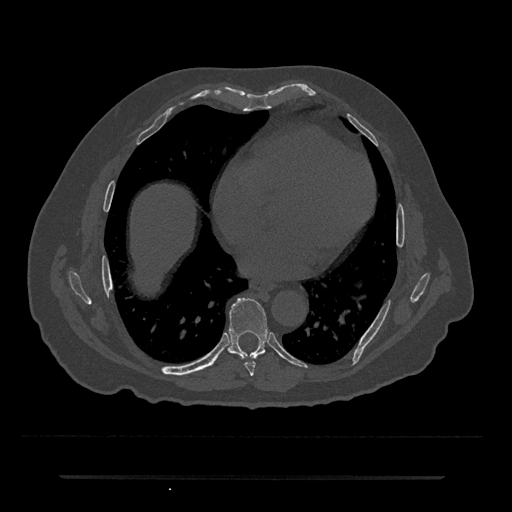
CT including the spine, one axial slice; slice 353 of 797 in the series (ordered by position); reconstruction kernel Br40s/3; 120 kVp; bone window (W 1800 / L 400 HU); 0.5 mm slice thickness; 512 × 512 image matrix. Male patient, age 69 years. From the clinical record (not read from this slice): primary cancer: prostate.
Annotated regions visible in this slice (semi-automatically segmented with operator editing):
- T7 vertebra: bounding box <245,362,256,376> (left, top, right, bottom; pixels)
- T8 vertebra: <227,298,268,359>